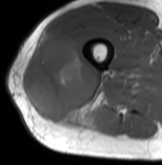
MRI of an extremity soft-tissue mass, one axial slice. Position 42 of 61 along the scan axis. MR volume resampled by the dataset authors to the PET/CT grid (not the native acquisition matrix). 3.27 mm slice thickness. 162 × 165 image matrix, field of view 158 × 161 mm. Male patient. From the clinical record (not read from this slice): histological type: poorly differentiated synovial sarcoma; grade: high; site of the primary tumour: right buttock.
Outlined on this slice (expert contour drawn on MRI and transferred to this co-registered scan by the dataset authors):
- gross tumour volume including surrounding oedema: bounding box <22,33,101,126> (left, top, right, bottom; pixels)
- gross tumour volume (mass): <22,33,99,126>